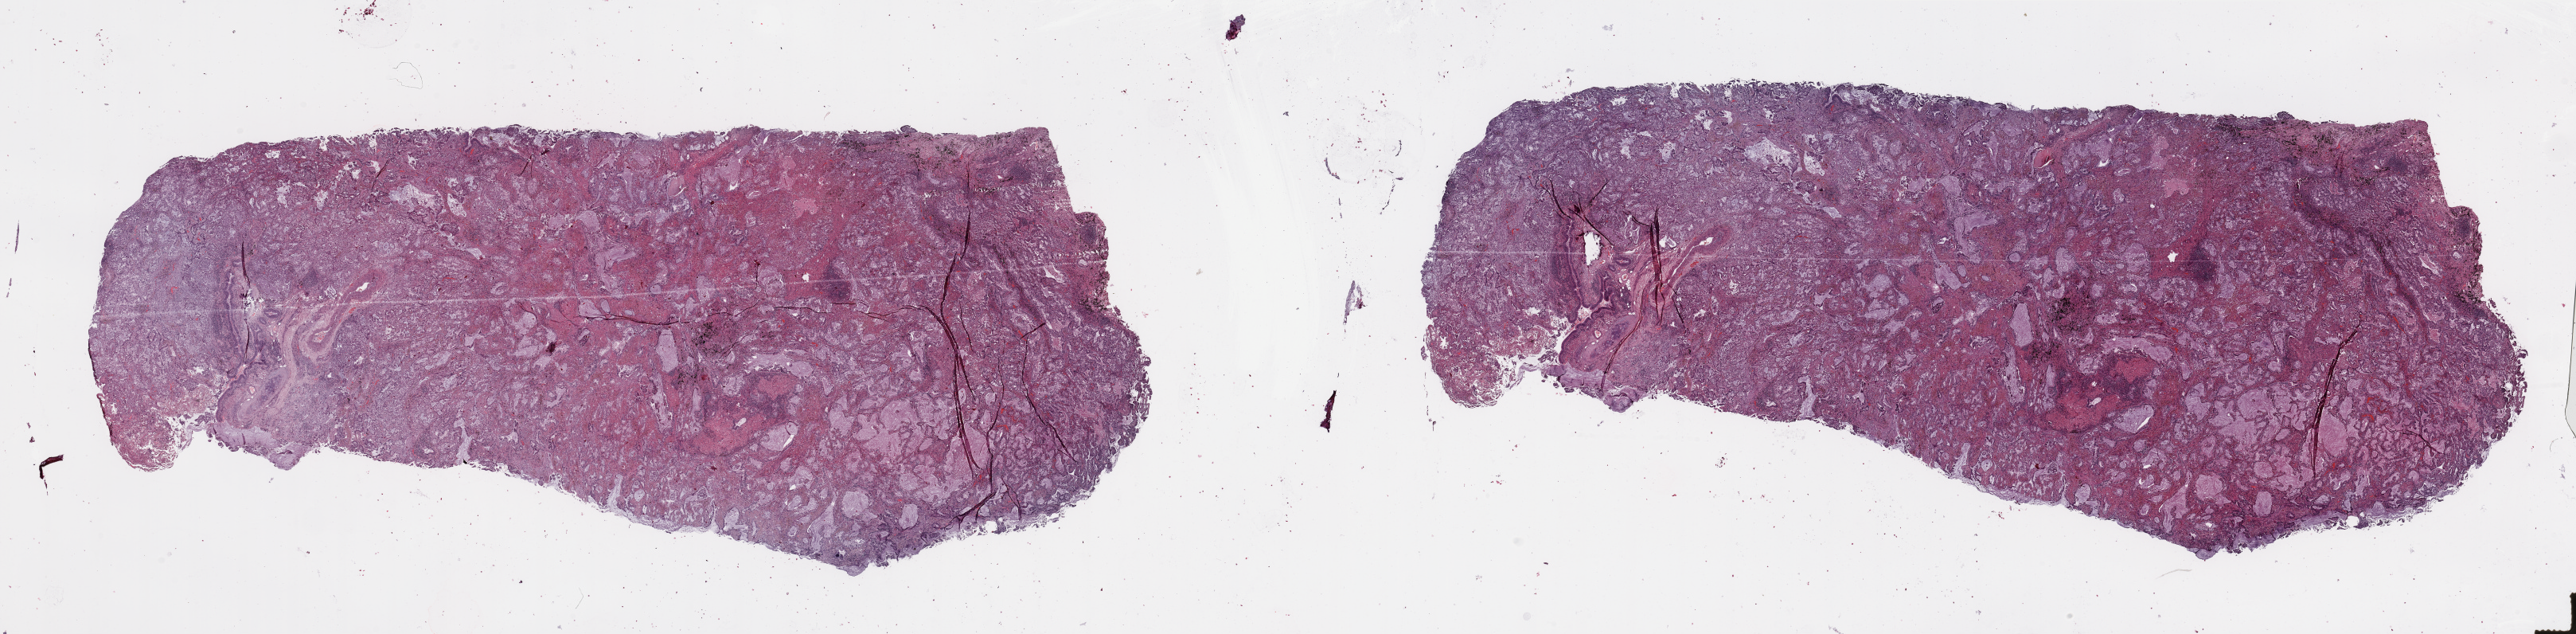
Digitized H&E tissue section (whole slide) — whole scanned area (about 51.2 x 12.6 mm, slide scanned at 20x) shown as a low-resolution overview. Lung, tumour tissue. Patient: male, age 64 years. Histologic grade: G2 (moderately differentiated).
Primary tumour site (as recorded): left lower lobe. Diagnosis: Adenocarcinoma, NOS. AJCC pathologic stage: IIA.